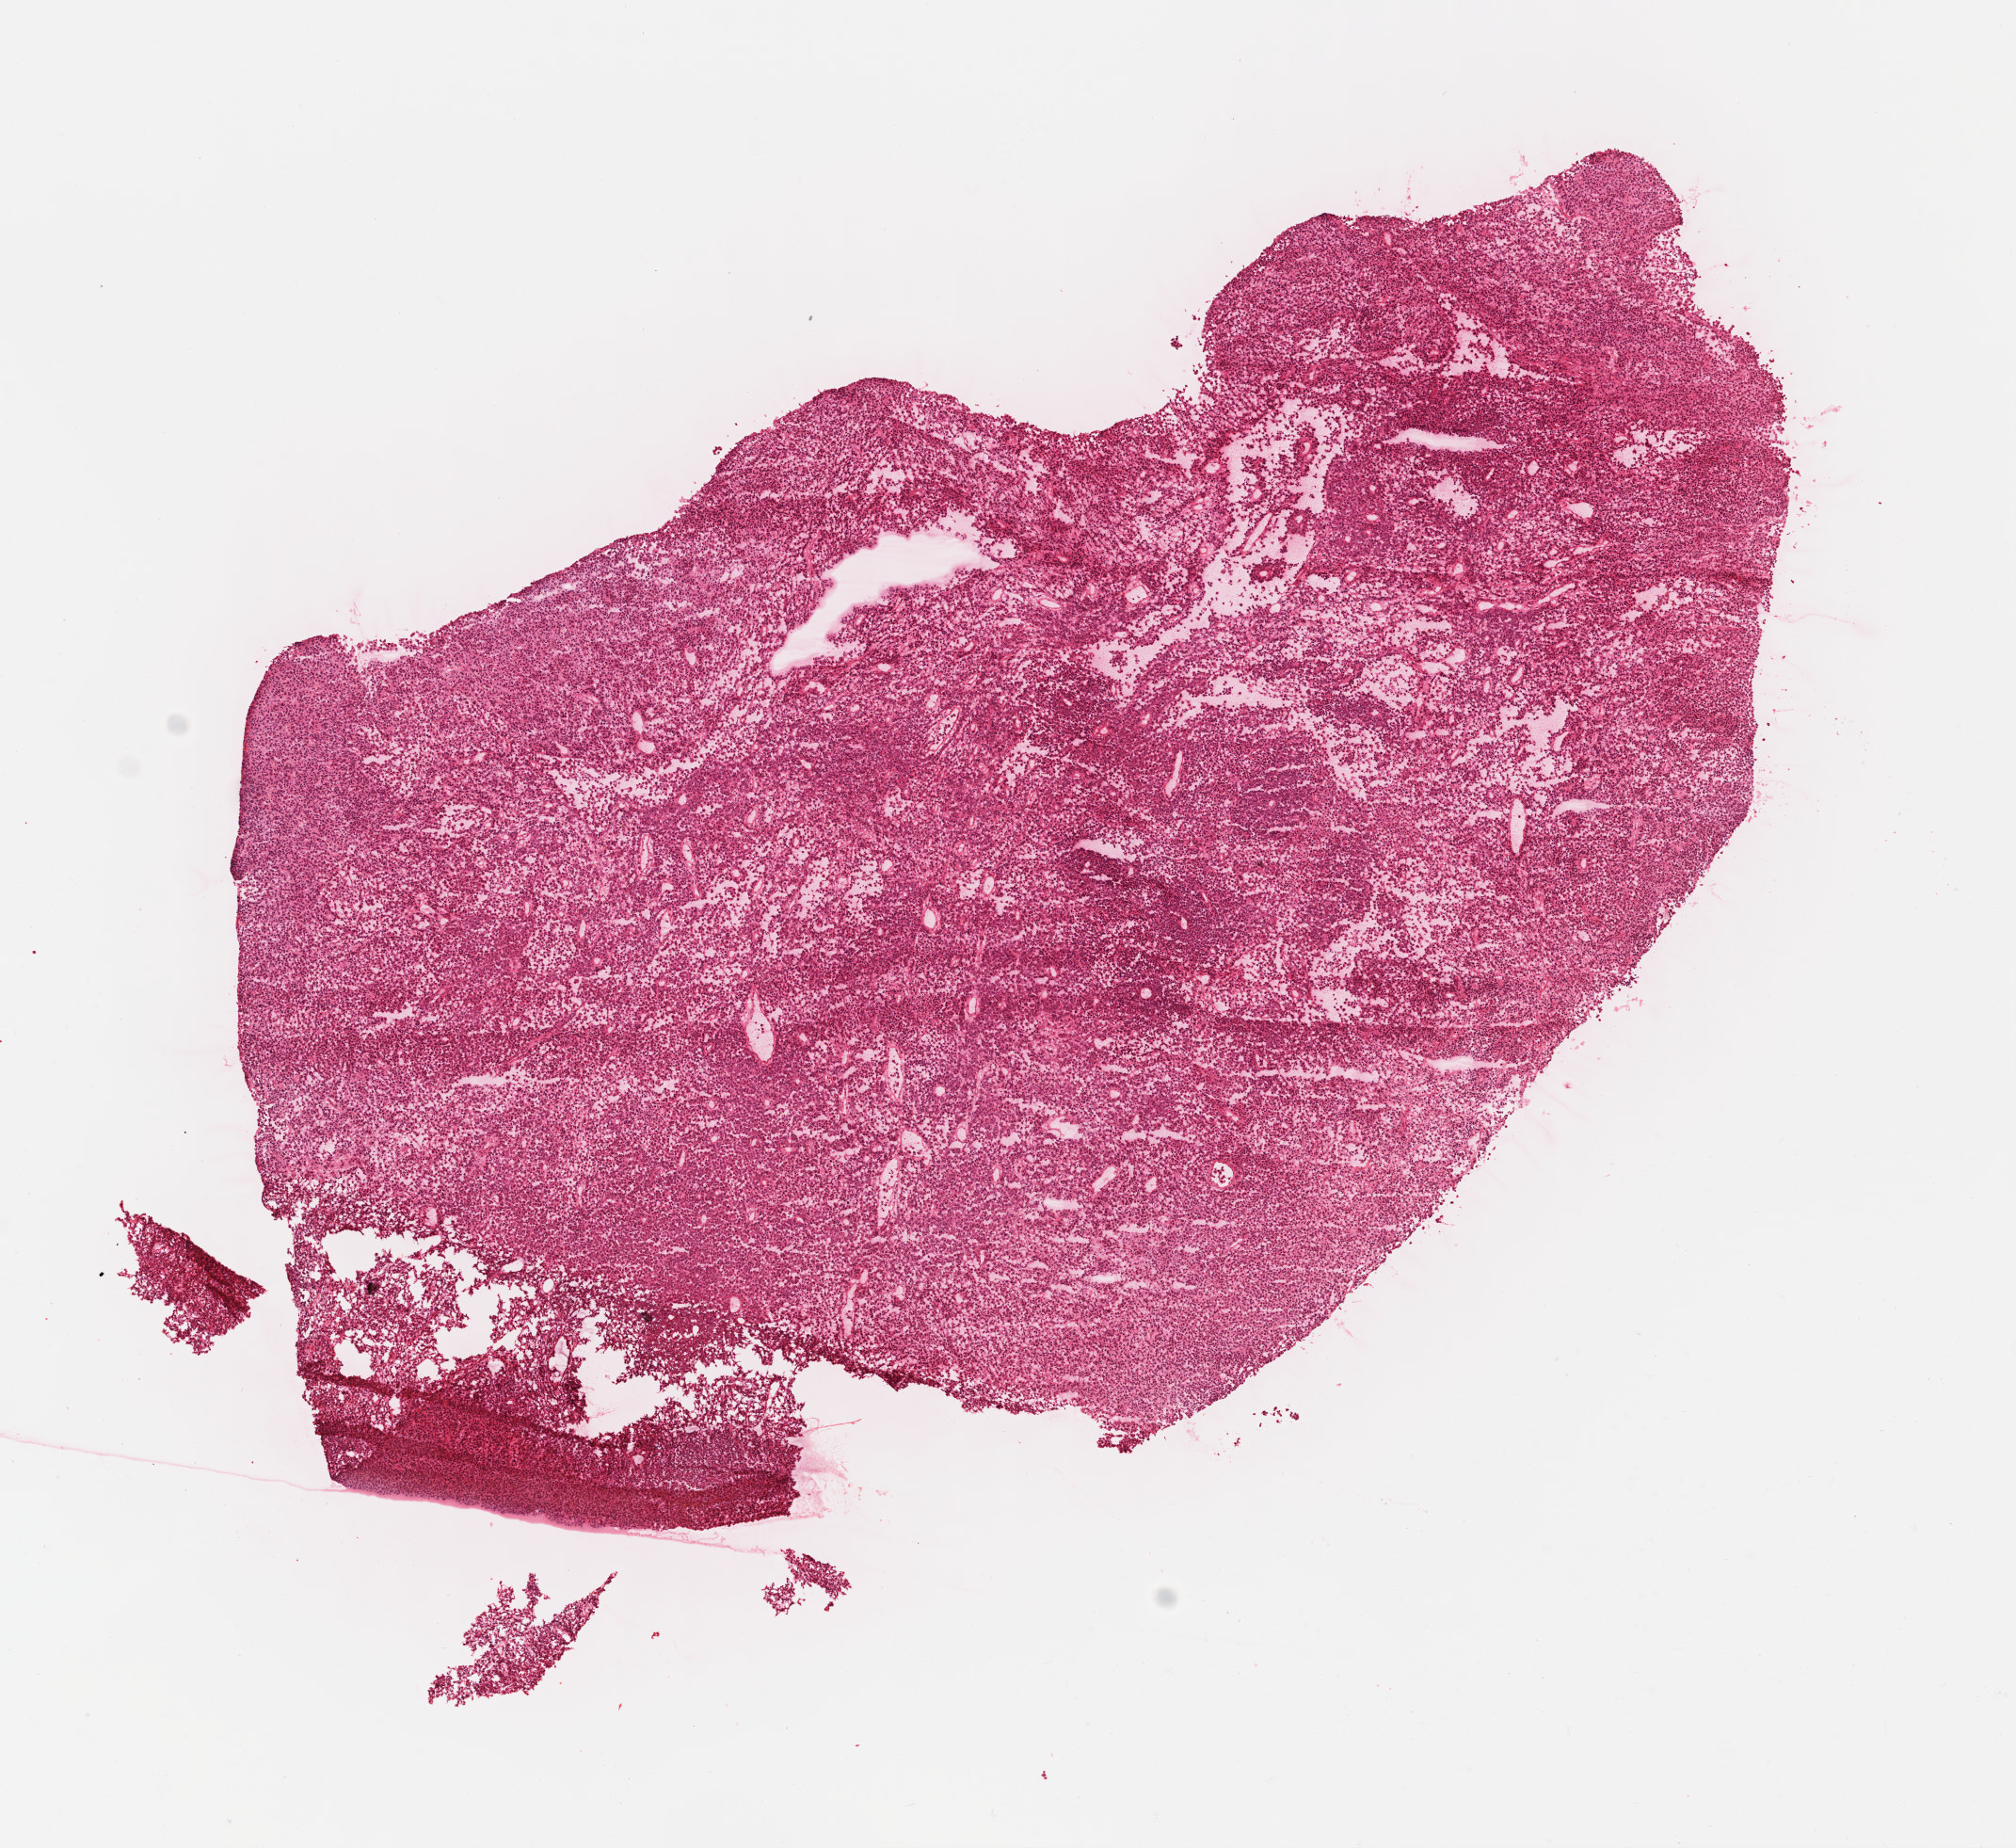
H&E-stained whole-slide image — low-resolution overview of the scanned area, about 8.4 x 7.7 mm (slide scanned at 40x). Formalin-fixed paraffin-embedded (FFPE) diagnostic section. Sample: primary tumour, skin. Patient: male, age at initial diagnosis 48 years.
Histologic diagnosis: Malignant melanoma, NOS.